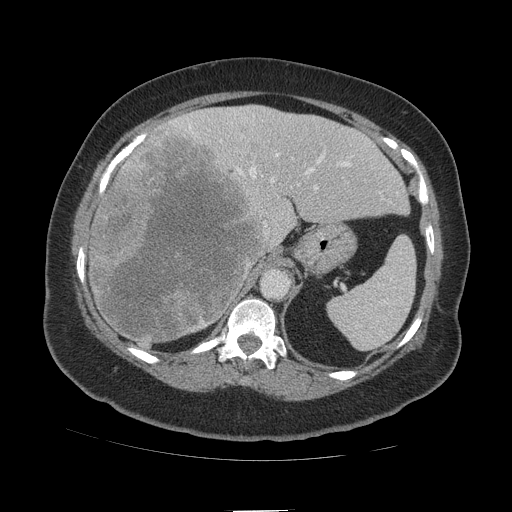
Contrast-enhanced abdominal CT (liver protocol), one axial slice. Reconstruction kernel STANDARD. Soft-tissue window (W 400 / L 40 HU). 2.5 mm slice thickness. 512 × 512 image matrix, field of view 420 × 420 mm. From the clinical record (not read from this slice): diagnosis: hepatocellular carcinoma (patient treated with transarterial chemoembolisation; whether this scan precedes or follows treatment is not stated here); TNM stage (as recorded): Stage-IVB.
Annotated regions visible in this slice (semi-automatic segmentation, software-assisted and operator-edited):
- liver parenchyma outside the tumour (the mass and vessels are separate outlines, so this box may not span the whole liver): bounding box [x1, y1, x2, y2] px = [88, 106, 408, 334]
- mass: [88, 130, 274, 351]
- liver vessels: [175, 114, 353, 190]